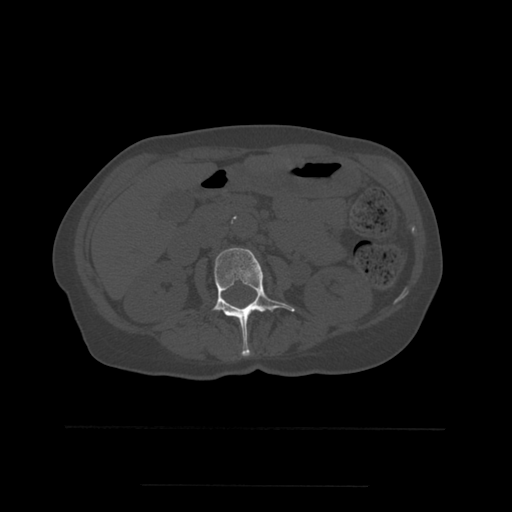
CT including the spine, one axial slice; slice 212 of 544 in the series (ordered by position); bone window (W 1800 / L 400 HU); 512 × 512 image matrix, field of view 350 × 350 mm. Patient age 58 years. Case-level facts recorded for this patient, not image findings: primary cancer: lung.
Structures marked on this image (semi-automatic segmentation, software-assisted and operator-edited):
- L2 vertebra: bounding box <212,248,295,357> (left, top, right, bottom; pixels)